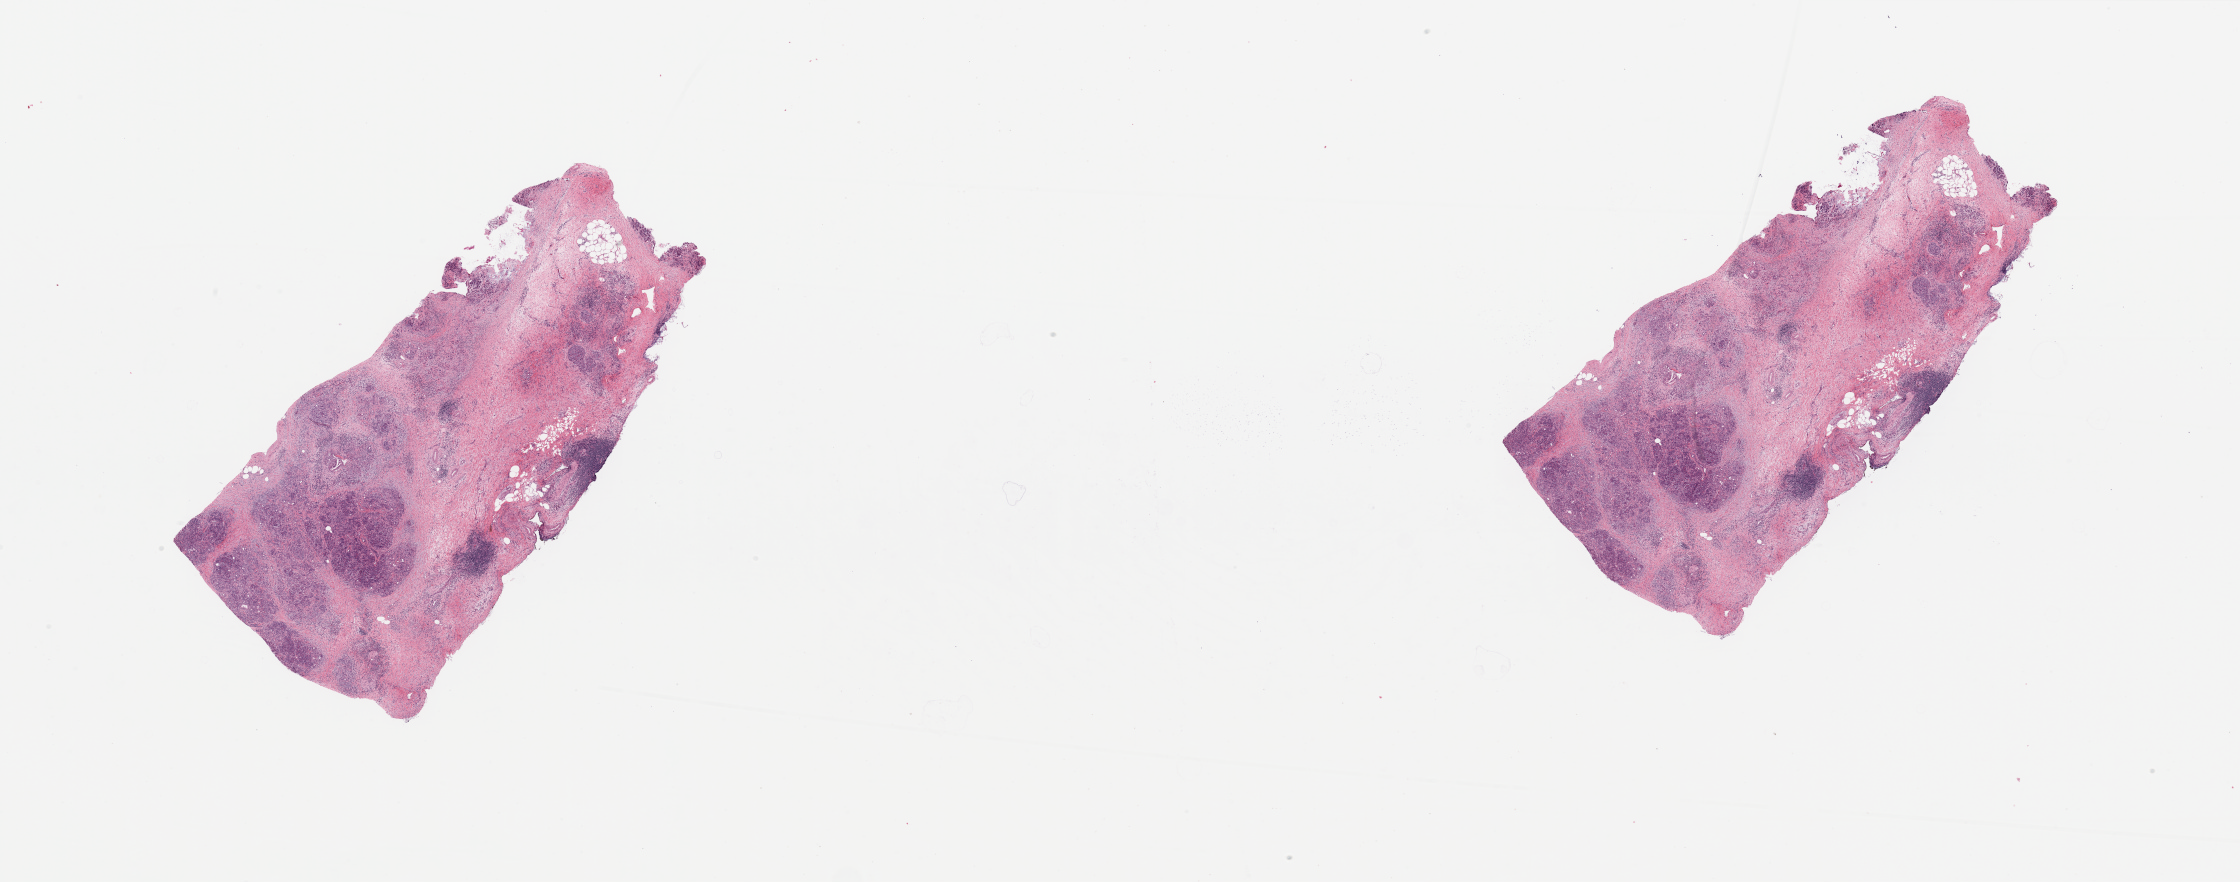
Whole-slide histology image, H&E, shown as a low-resolution overview of the whole scanned area (about 35.4 x 14.0 mm, slide scanned at 20x), pancreas, tumour tissue. 68-year-old male patient.
* primary tumour site (as recorded): tail
* patient diagnosis (cohort enrolment): ductal adenocarcinoma (pancreas)